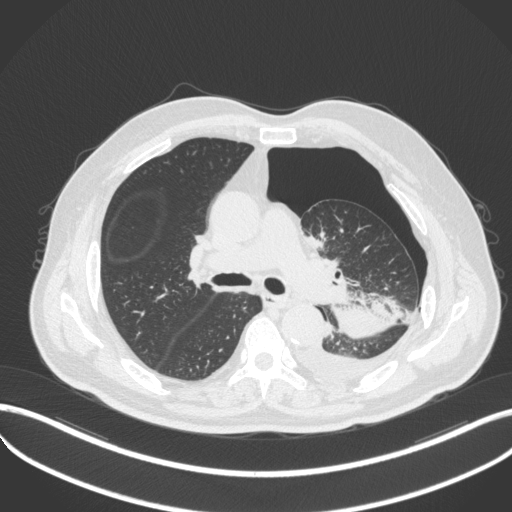
Chest CT, one axial slice; slice 318 of 466 in the series (ordered by position); reconstruction kernel B31f; 120 kVp; lung window (W 1500 / L -600 HU); 1 mm slice thickness; 512 × 512 image matrix, field of view 400 × 400 mm. Male patient, age 76 years. From the clinical record (not read from this slice): clinical TNM (as recorded): T3 N0 M1b.
Structures marked on this image (rectangle marked by the reading radiologist):
- lung tumour (recorded histology: adenocarcinoma): box from (x=328, y=282) to (x=402, y=343) px